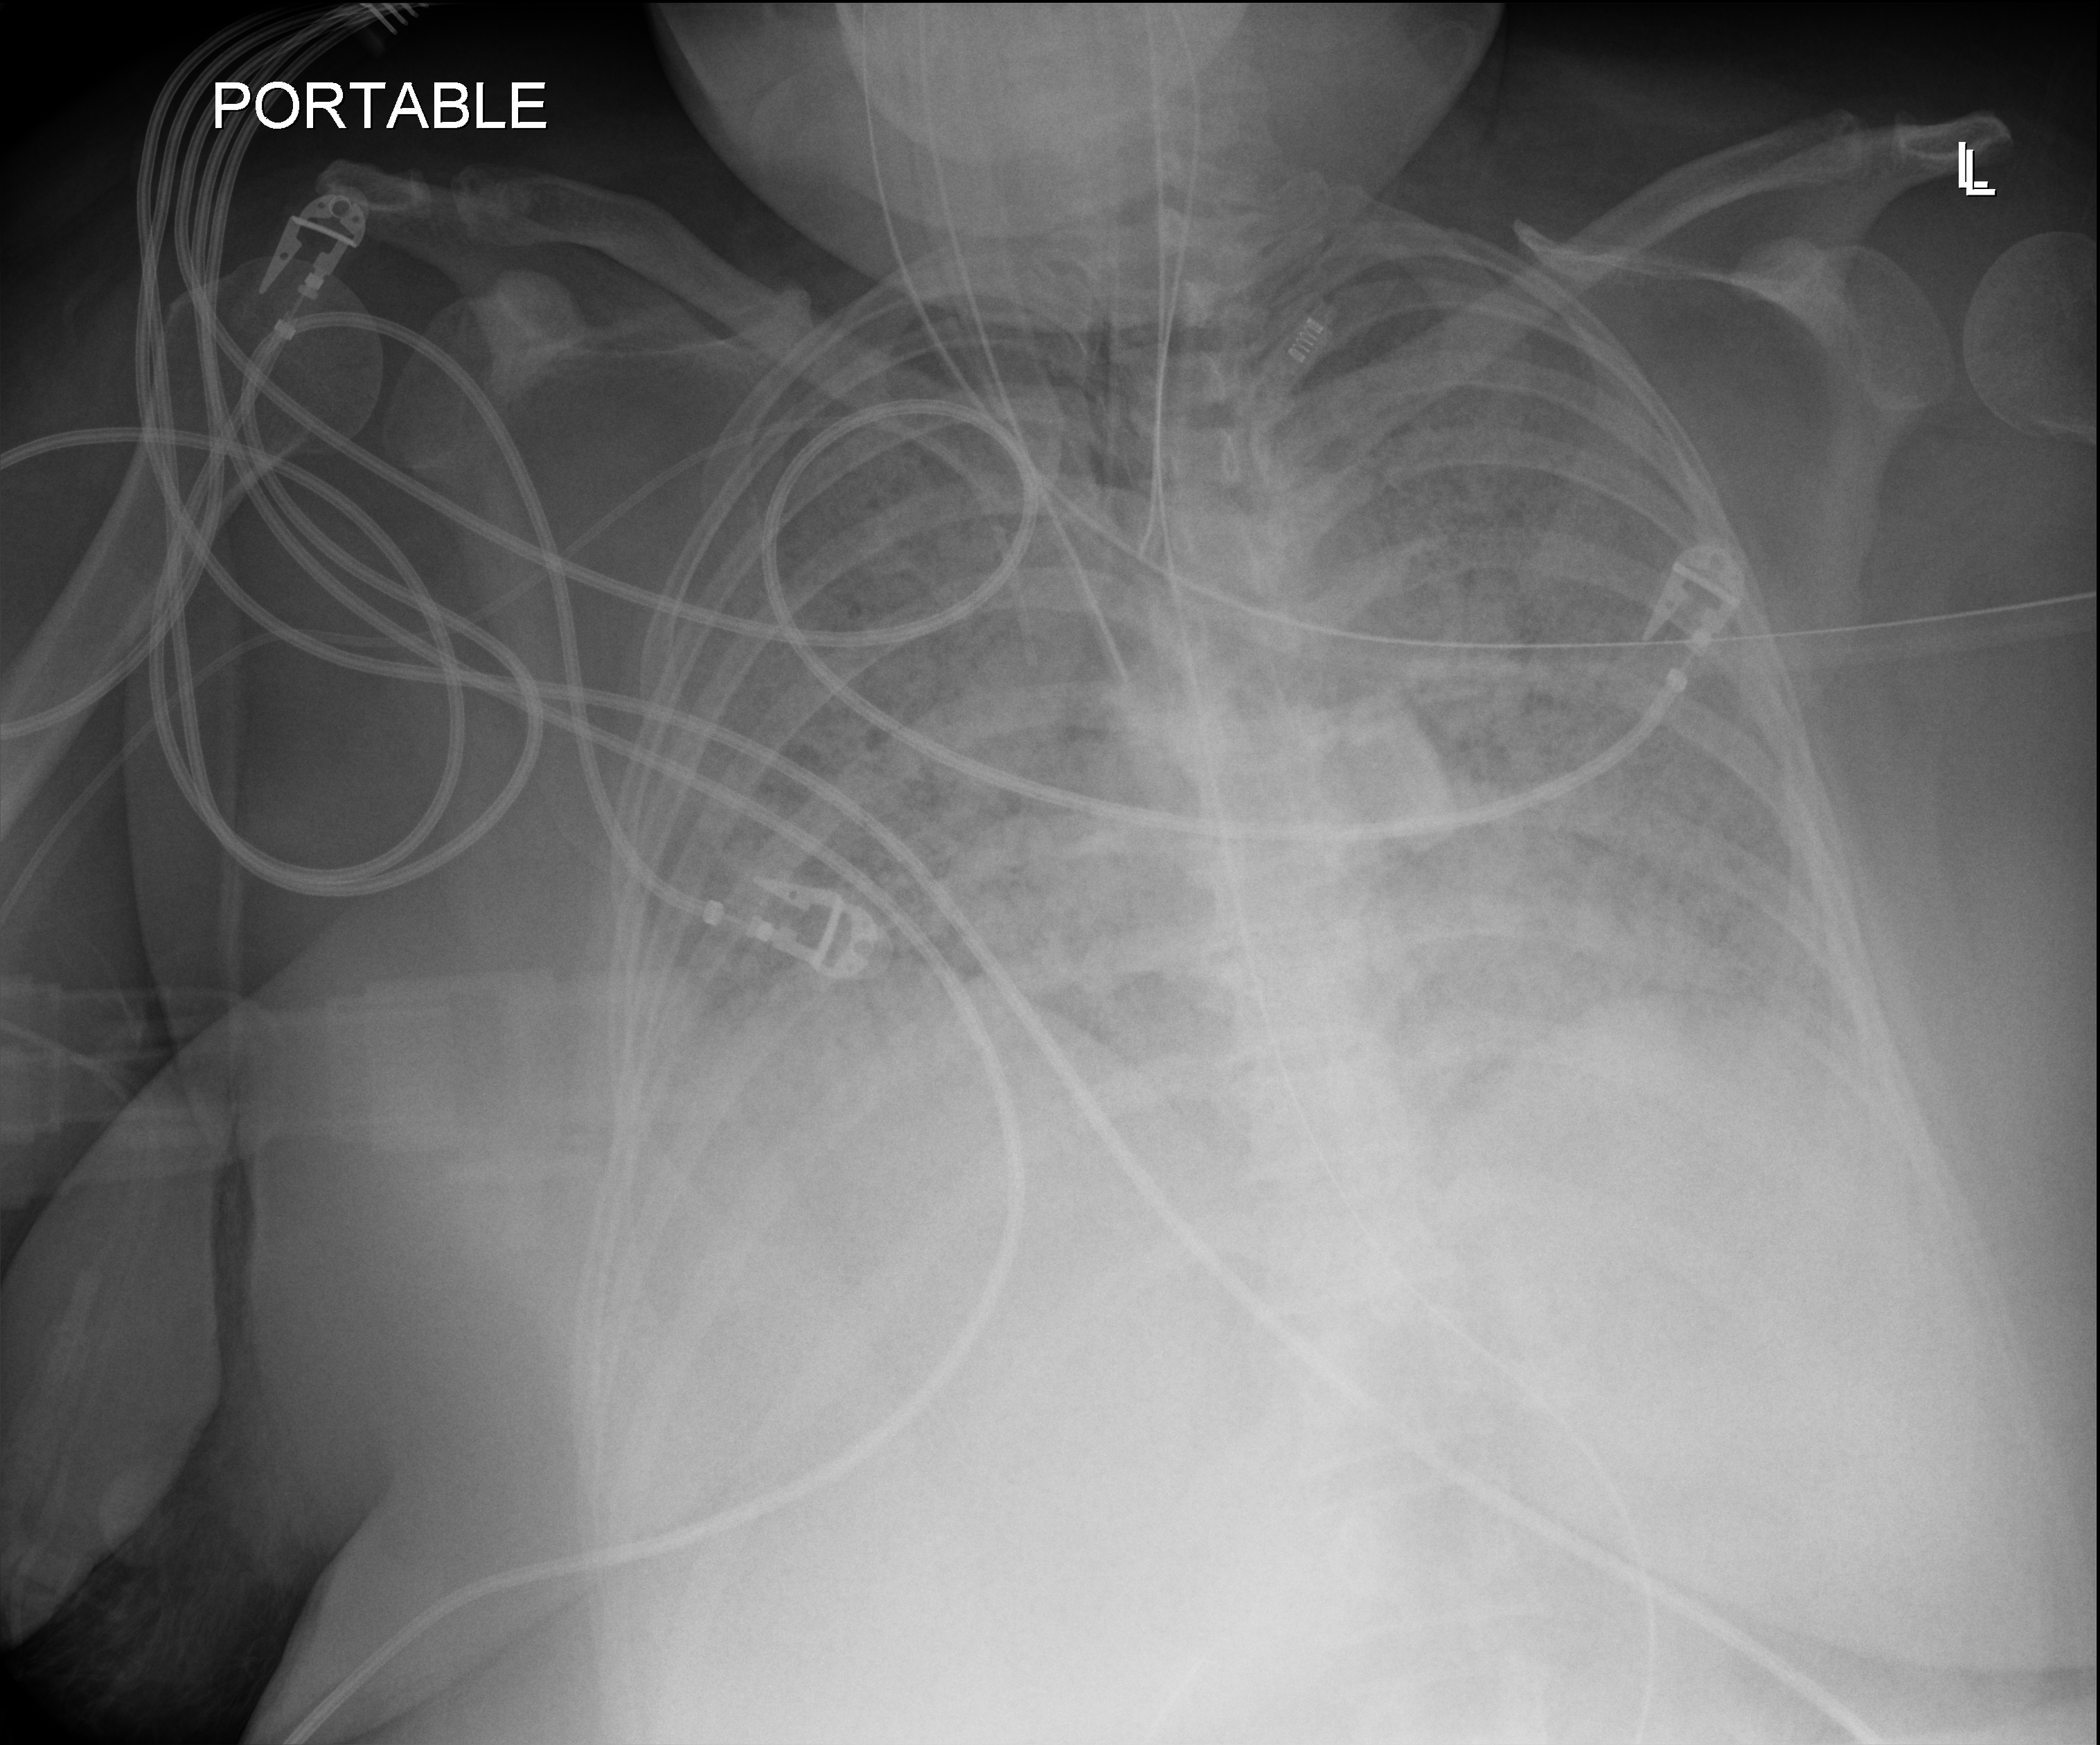
Bedside chest radiograph (digital radiography), anteroposterior (AP) projection. Female patient hospitalised with COVID-19, age 18–59 years.
From the hospital-stay record, not from the radiograph (when in the stay this image was taken is not recorded):
- mechanically ventilated during this hospital stay: yes
- admitted to intensive care during this hospital stay: yes
- length of hospital stay: 95 days